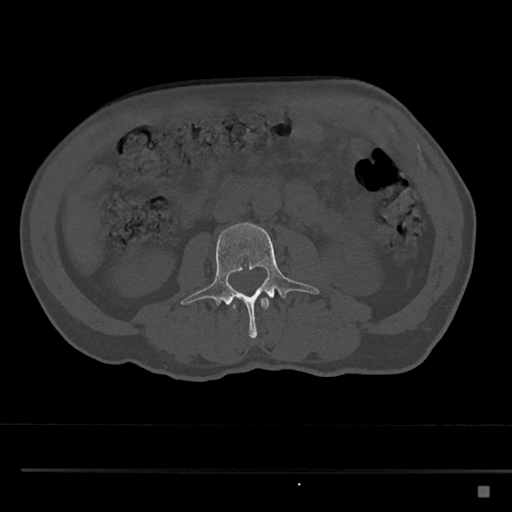
CT including the spine, one axial slice. Slice 703 of 797 in the series (ordered by position). 120 kVp. Bone window (W 1800 / L 400 HU). 0.5 mm slice thickness. 512 × 512 image matrix, field of view 391 × 391 mm. Patient: male, 59 years. From the clinical record (not read from this slice): primary cancer: prostate.
Annotated regions visible in this slice (semi-automatic segmentation, software-assisted and operator-edited):
- L2 vertebra: bounding box <228,298,269,309> (left, top, right, bottom; pixels)
- L3 vertebra: <181,222,320,340>